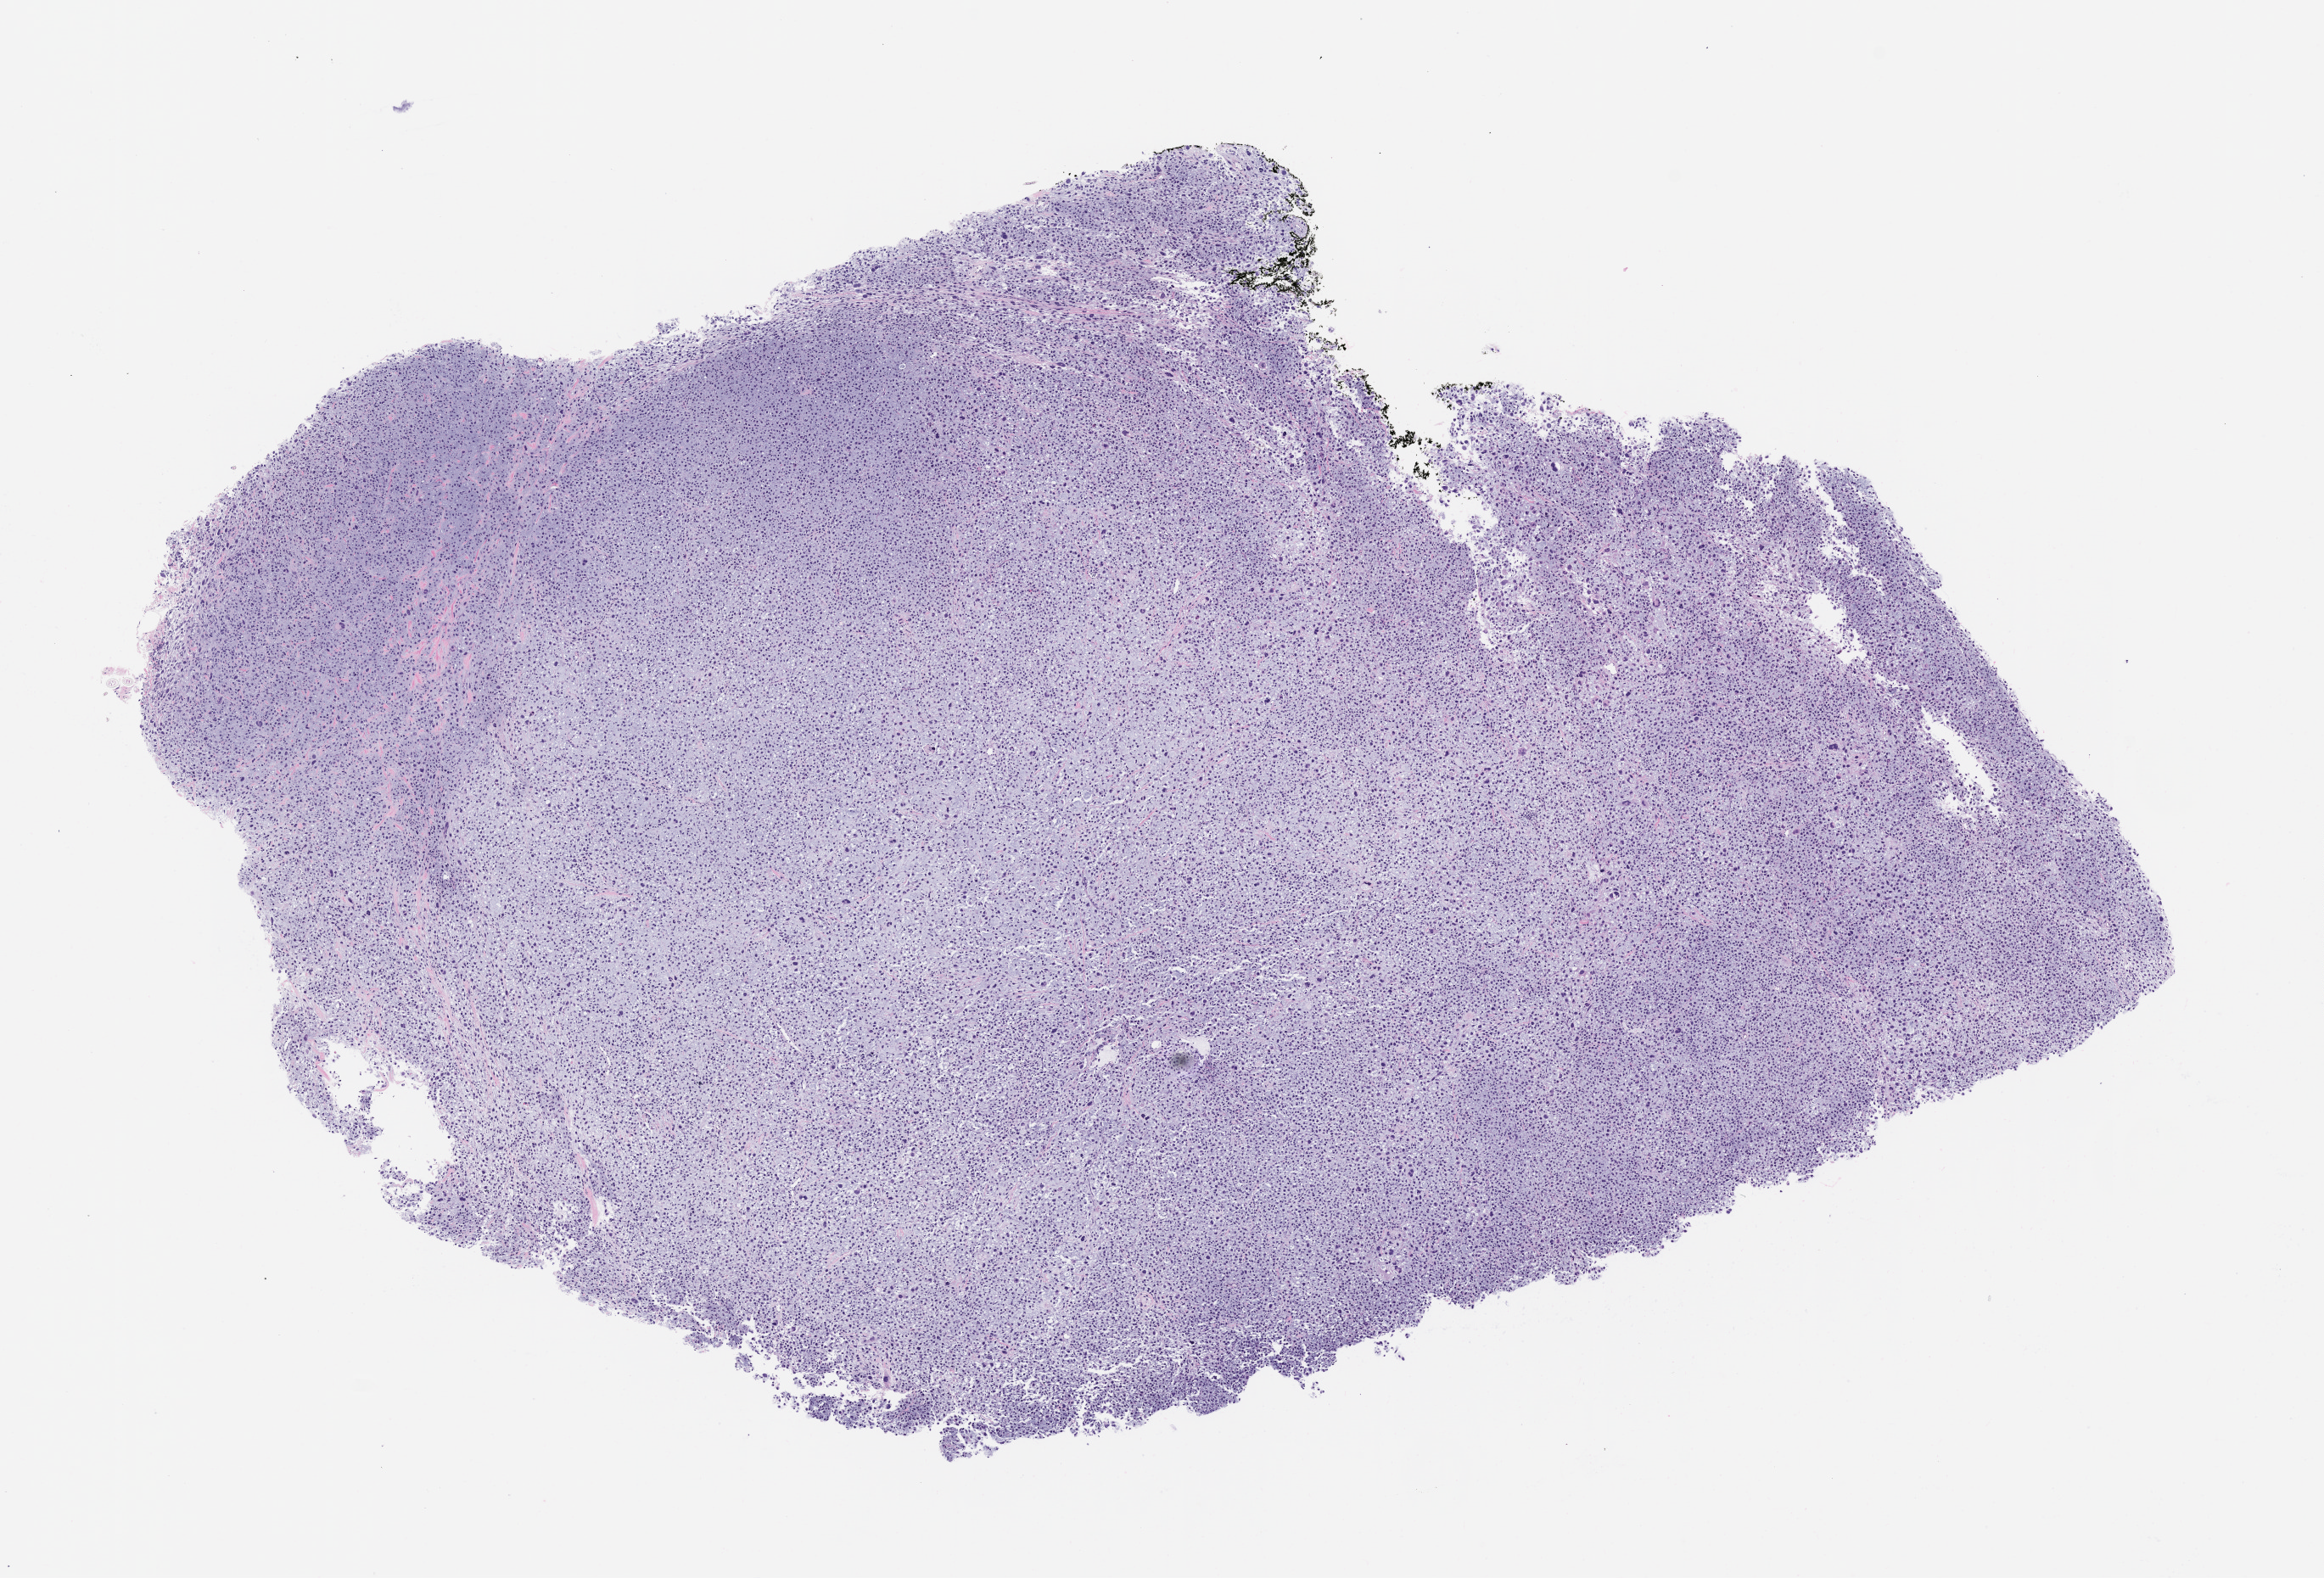
Whole-slide image, H&E: patient-derived xenograft (human tumor grown in a mouse), passage 1, low-resolution overview of the scanned area, about 11.0 x 7.5 mm, FFPE section, originating tumor site category: musculoskeletal.
Originating patient diagnosis: Myxofibrosarcoma.